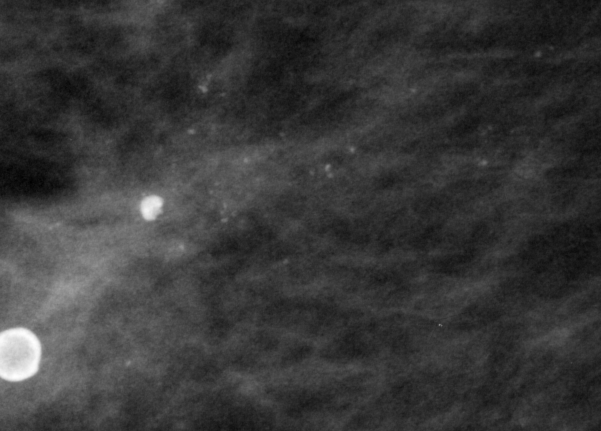
Cropped region of a digitized screen-film mammogram centred on a radiologist-marked abnormality; left breast; MLO view; BI-RADS breast density category 2 (scale 1–4).
Calcifications, morphology pleomorphic, distribution linear; BI-RADS assessment category 4; pathology (as recorded): malignant.